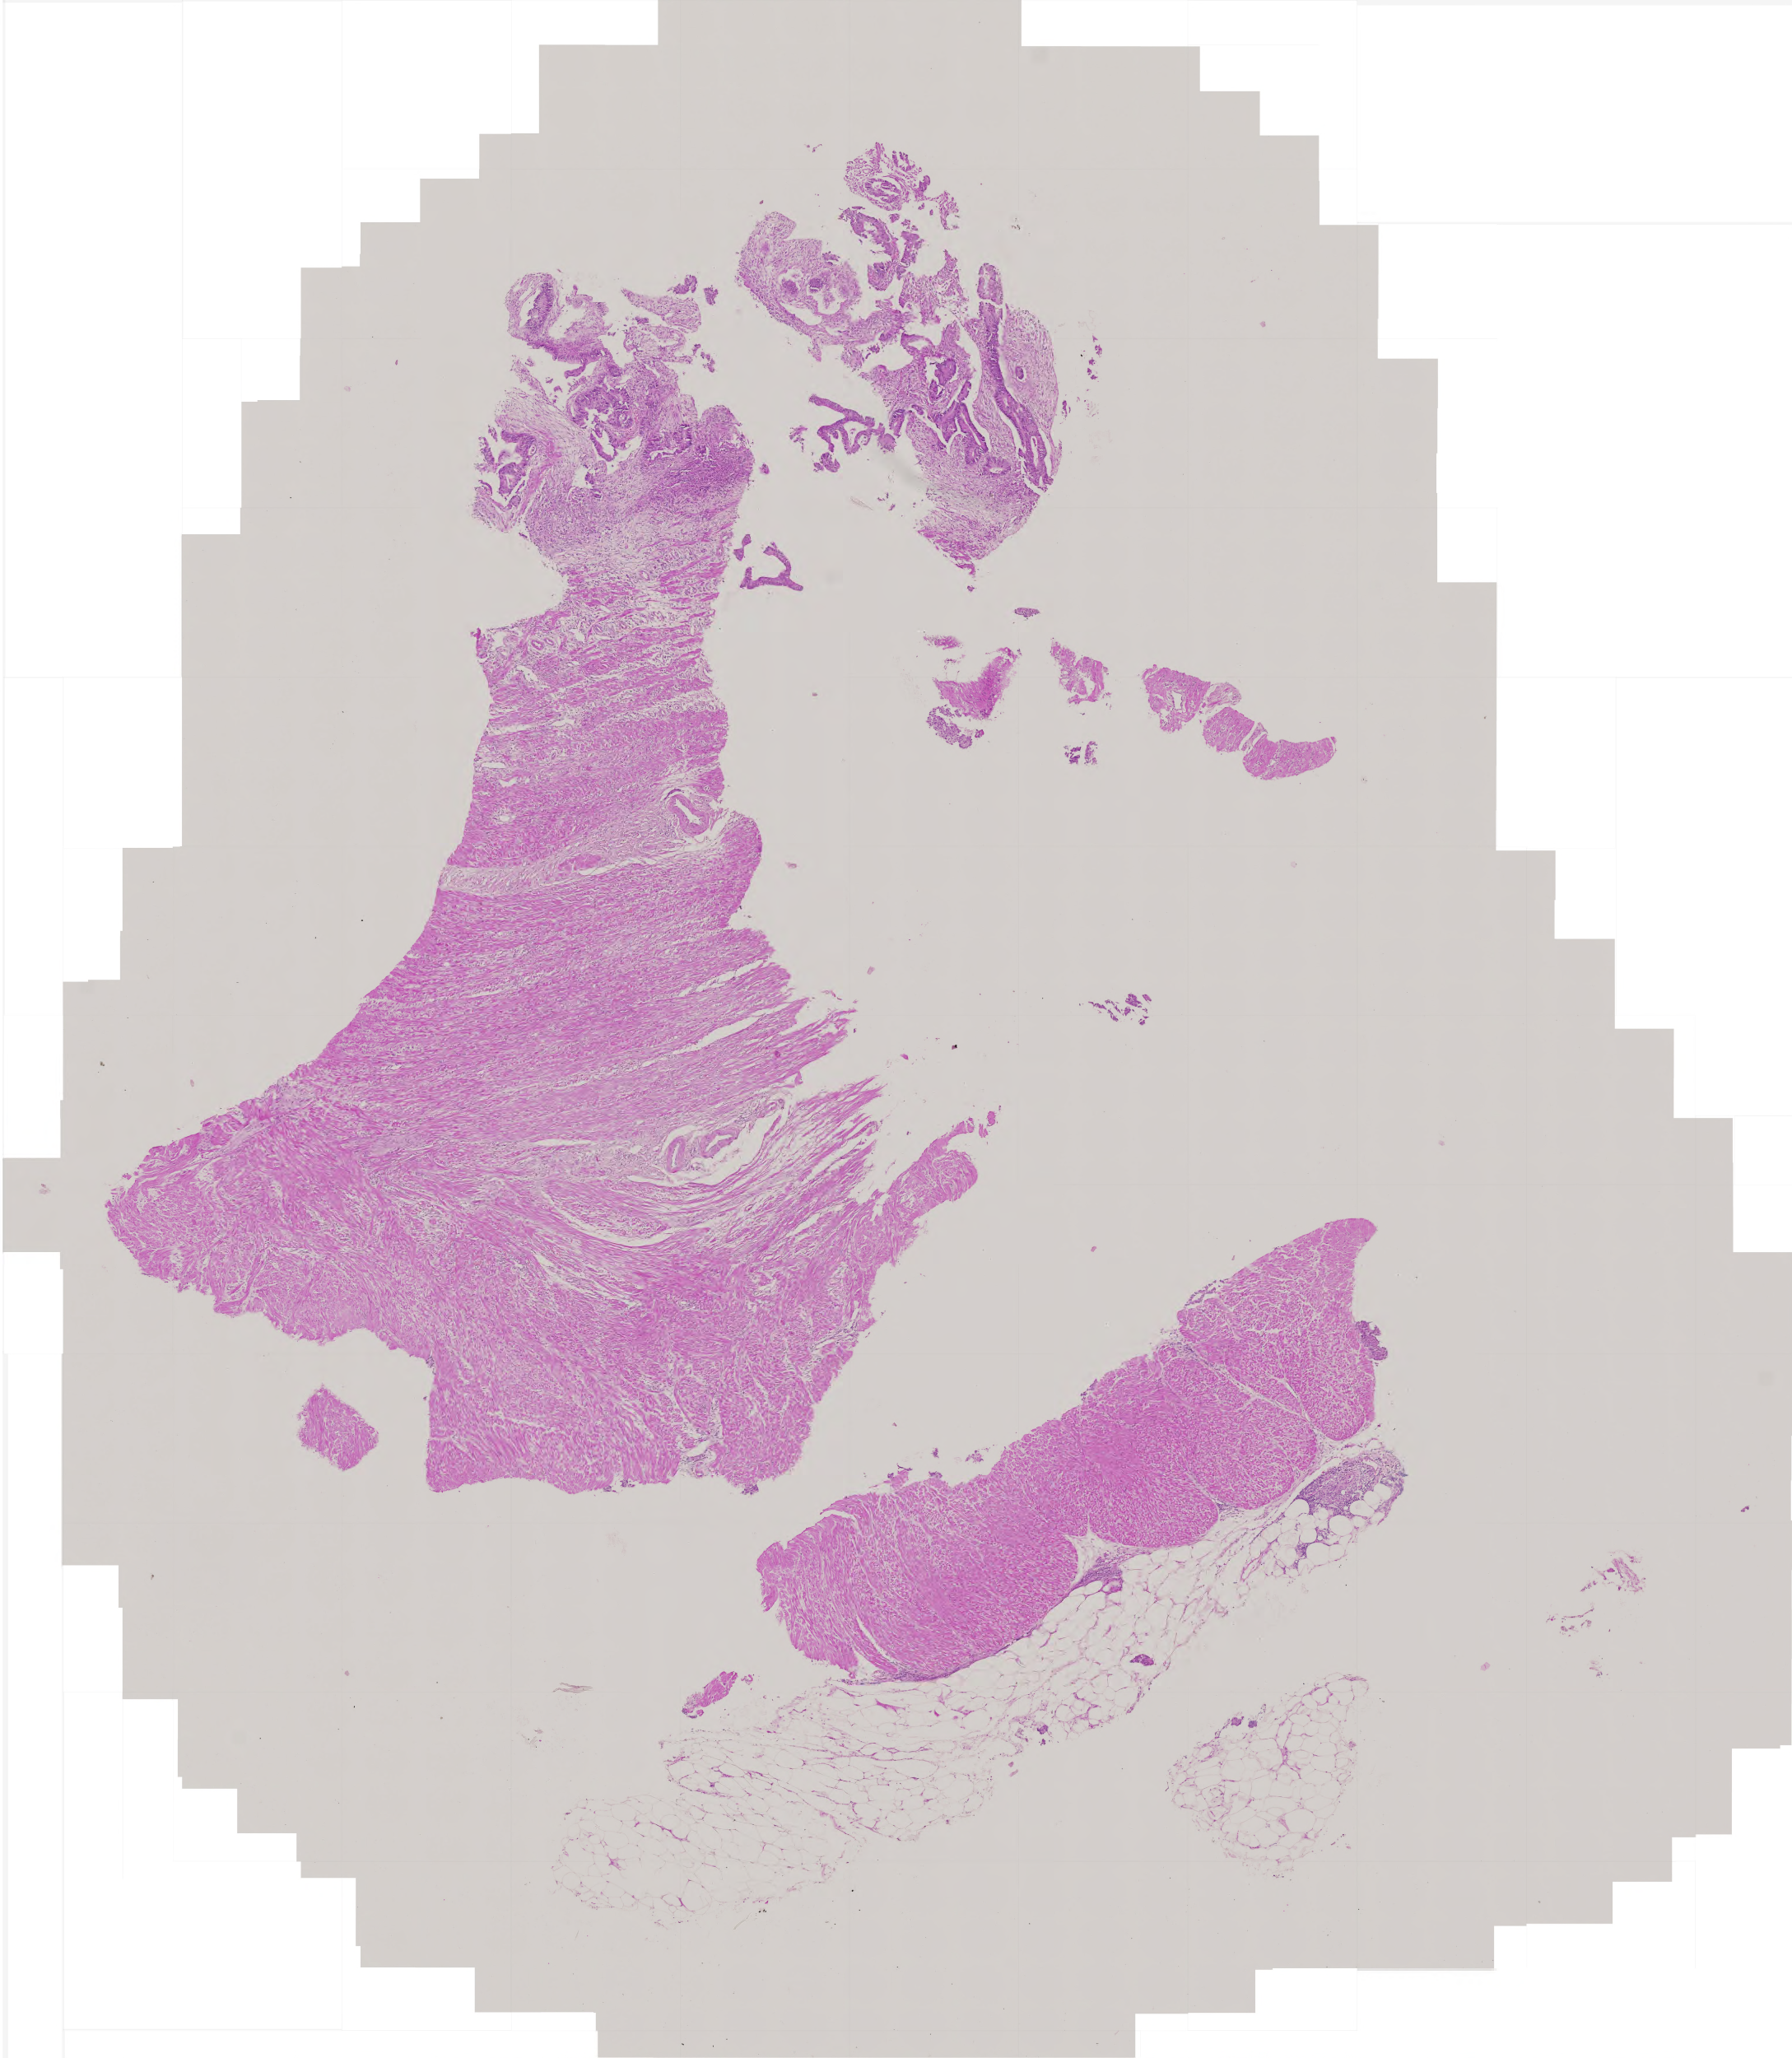
Digitized H&E-stained tissue section (whole slide) — low-resolution overview of the scanned area, about 4.4 x 5.0 mm, FFPE section, colon, primary tumour sample. Patient: male, age at initial diagnosis 75 years.
Pathologic diagnosis: Adenocarcinoma, NOS.